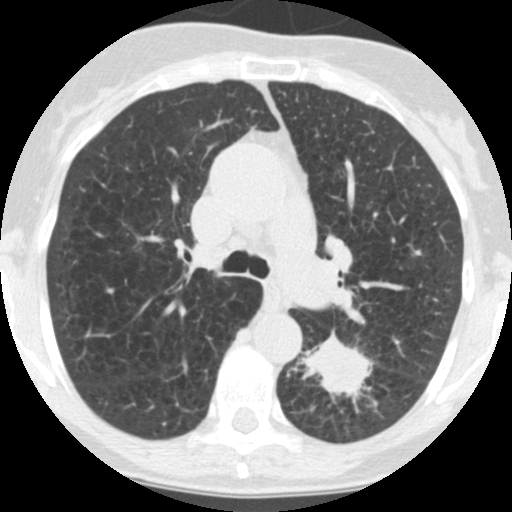
Low-dose screening chest CT, axial slice; third annual screen; lung window (W 1500 / L -600 HU); 2.5 mm slice thickness; standard (soft-tissue) reconstruction kernel (STANDARD); slice 57 of 171 in the series. Female participant, aged 71 years at enrolment. Current smoker at enrolment.
• Expert reader's lesion annotation, bounding box [x1, y1, x2, y2] px = [301, 329, 382, 411].
• The screening reader recorded 2 non-calcified nodules or masses ≥4 mm on this exam (left lower lobe, left lower lobe); which of them this box marks is not recorded.